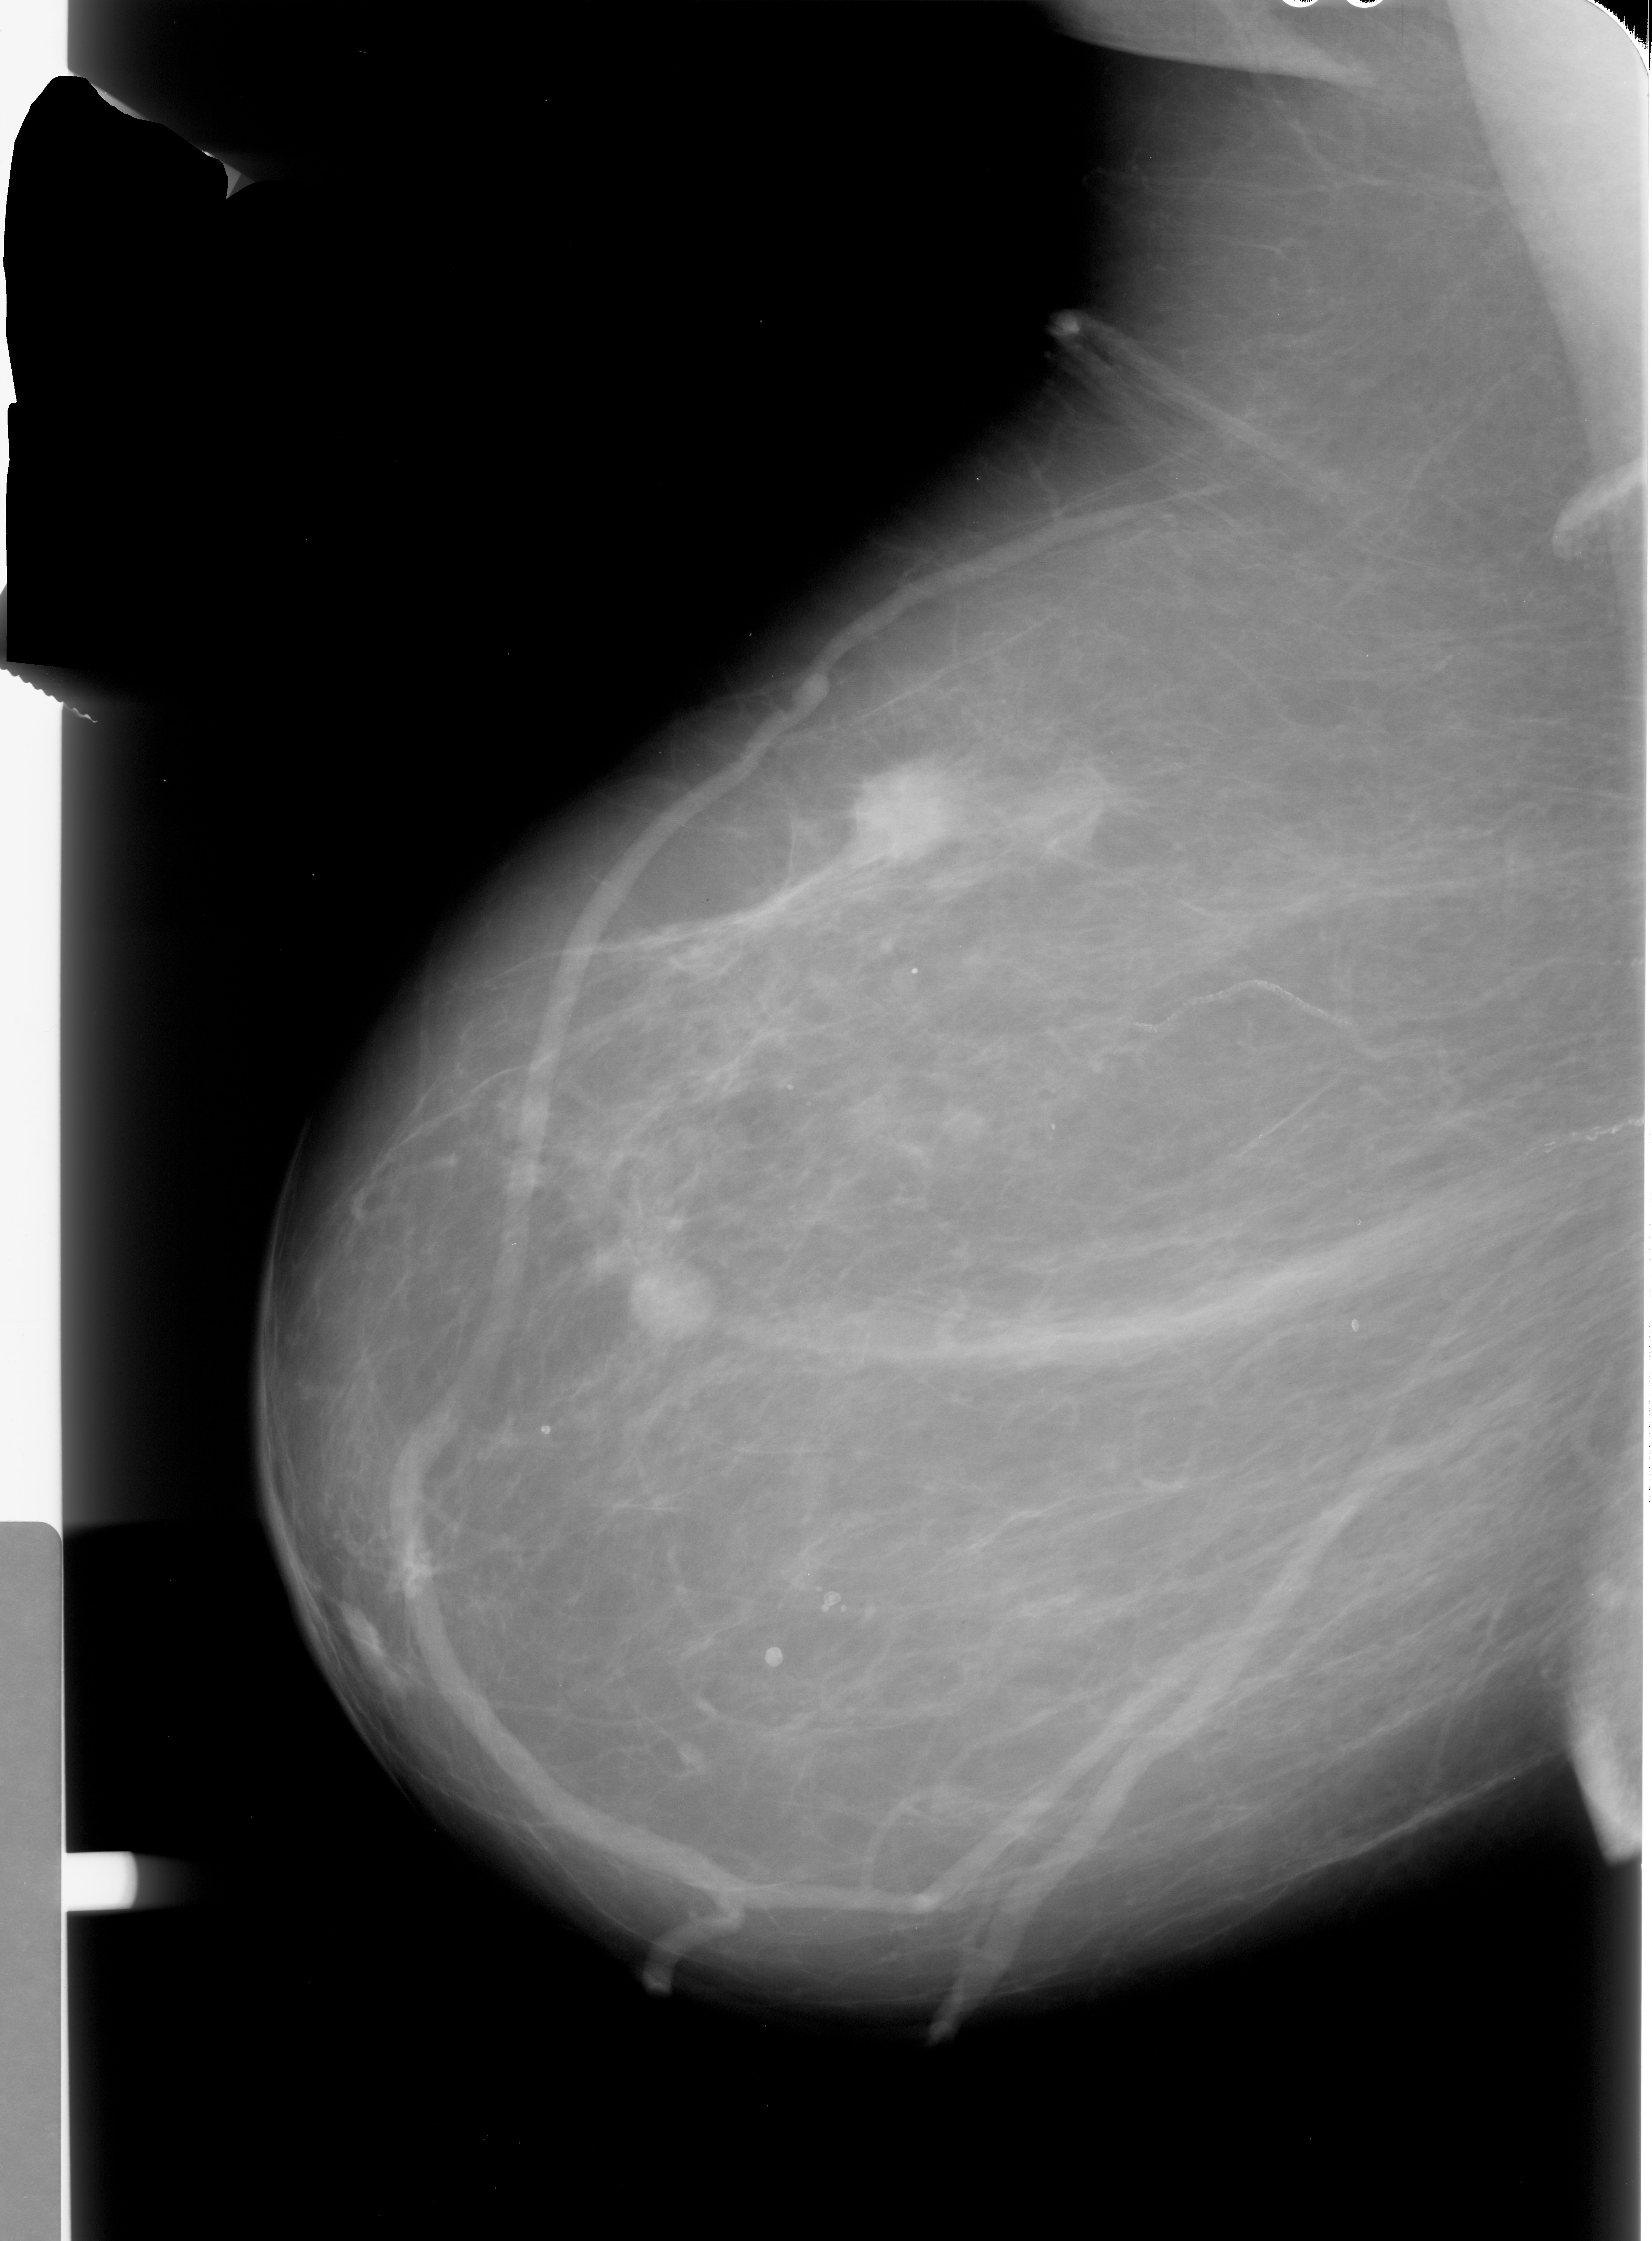
Digitized screen-film mammogram, left breast, MLO view.
Finding: mass, shape irregular, margins spiculated; BI-RADS assessment category 5; subtlety rating 5 on a 1 (subtle) to 5 (obvious) scale; pathology result (as recorded, not read from the image): malignant.